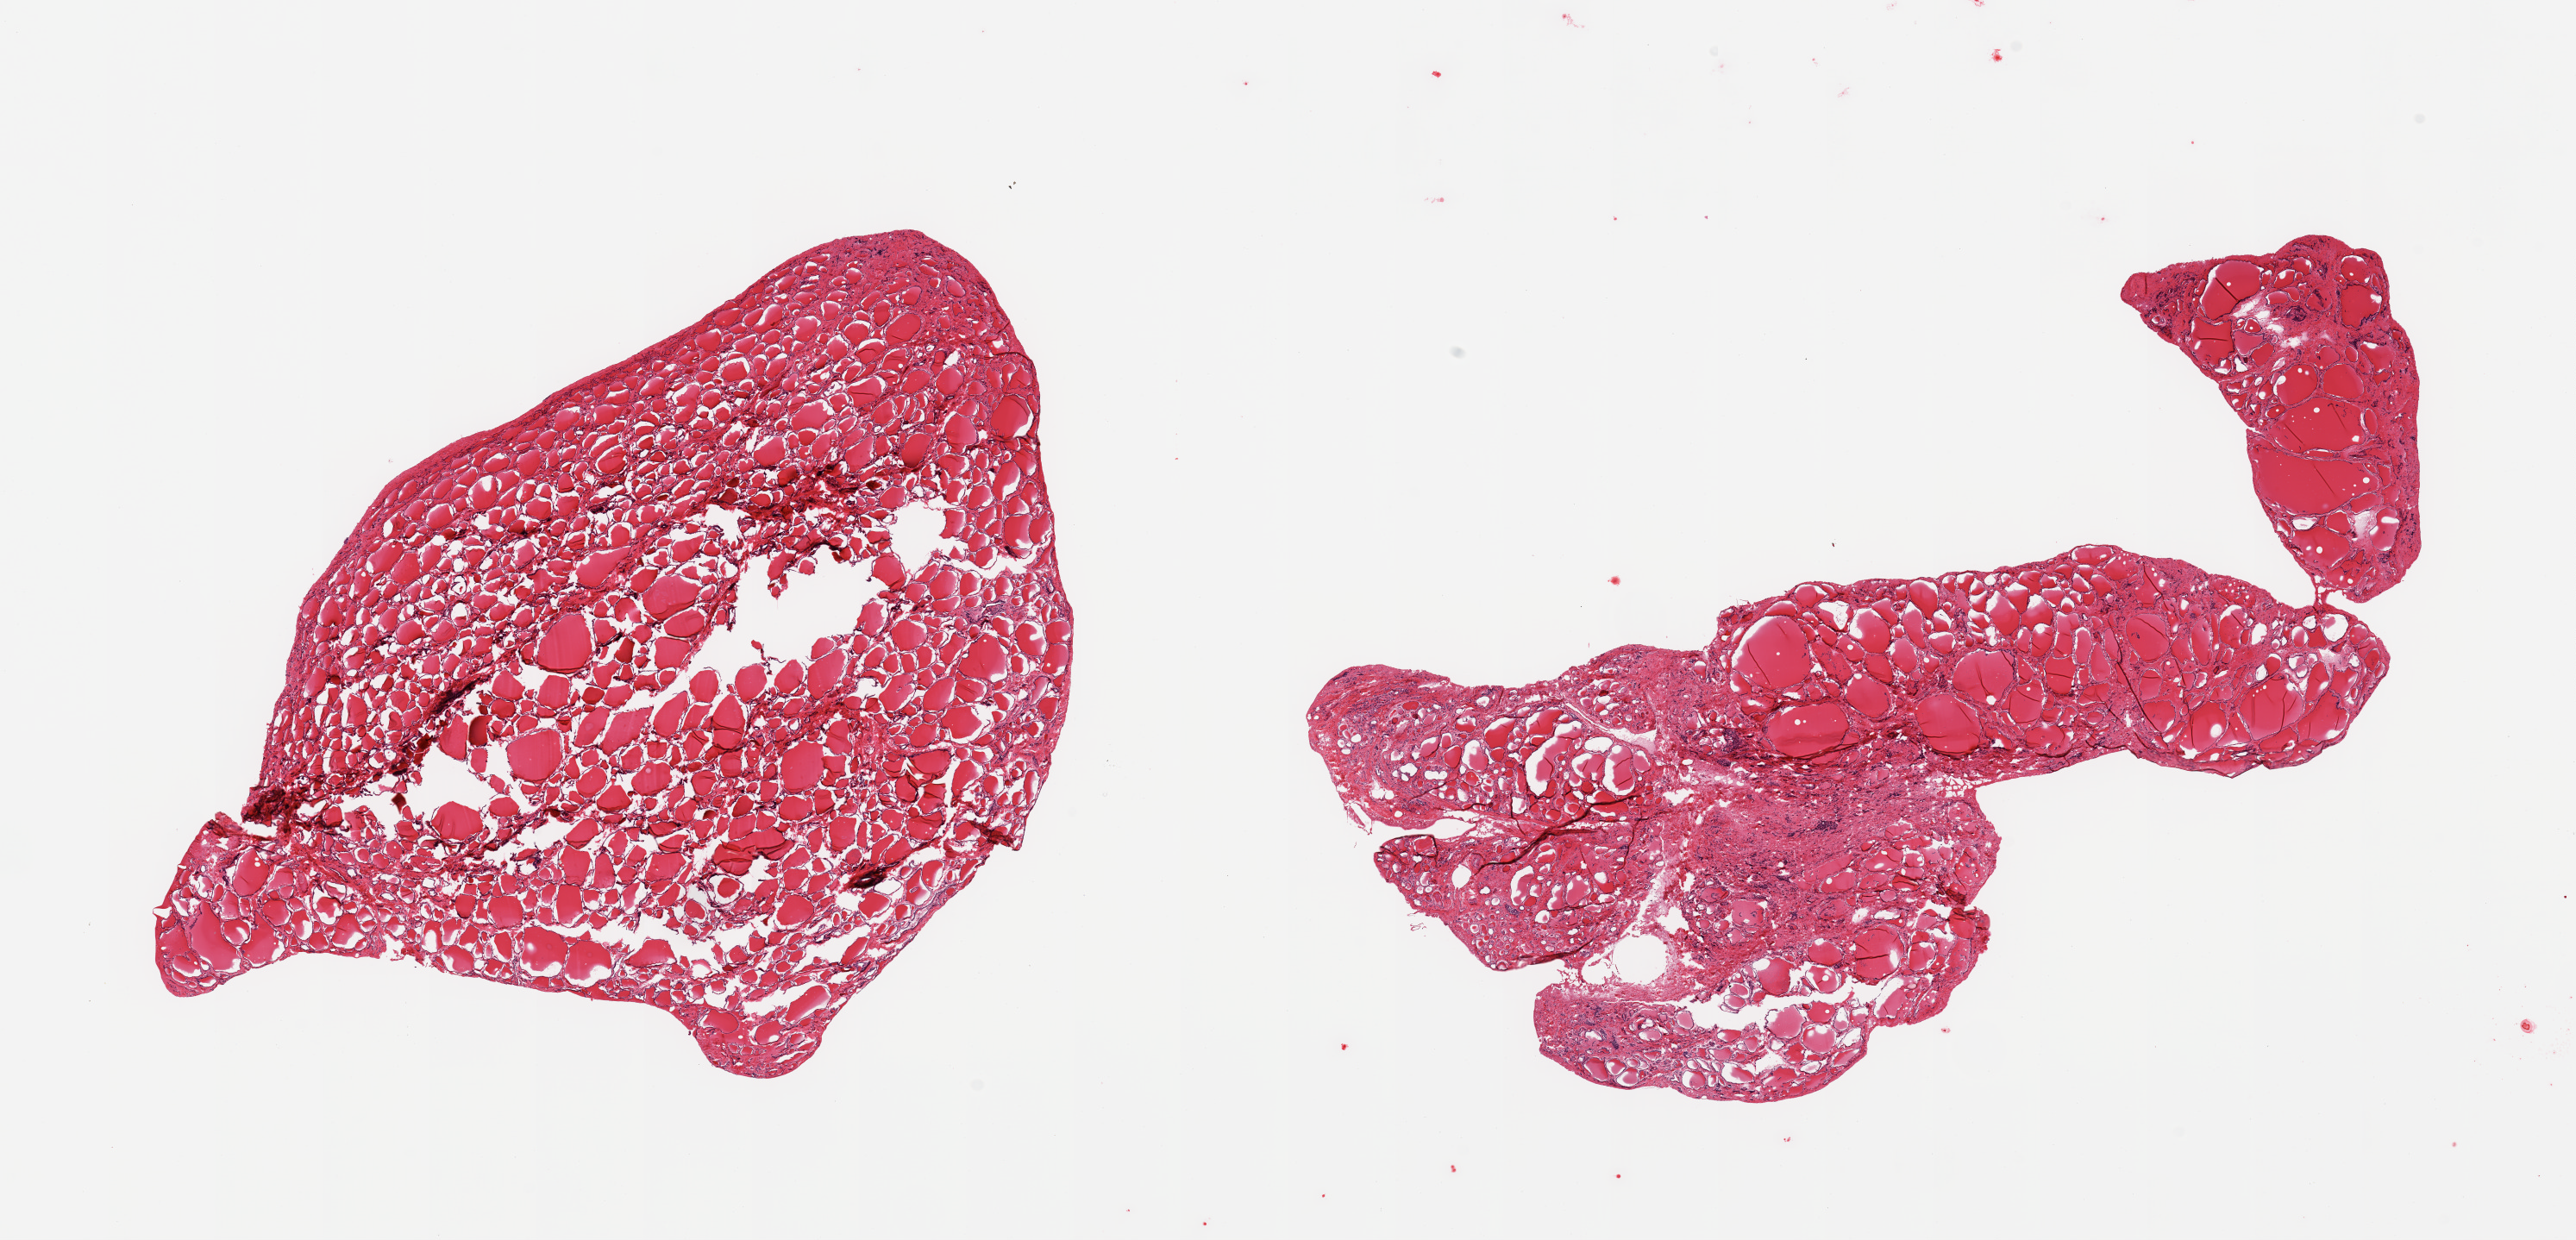
Digitized hematoxylin and eosin (H&E)-stained section, brightfield, whole scanned area (about 23.6 x 11.4 mm, slide scanned at 20x) shown as a low-resolution overview, PAXgene-fixed, paraffin-embedded tissue, target tissue: thyroid, tissue donor sample. Male donor.
Pathologist's review note for this sample: 2 pieces; some fibrosis and nodularity.